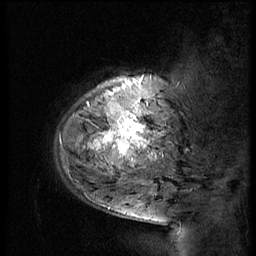
Breast MRI (dynamic contrast-enhanced), one sagittal slice; position 11 of 56 along the scan axis; 3 images stored at this slice position (order not interpretable as contrast timing); 1.5 T; TE 4.2 ms, TR 9 ms; 2.5 mm slice thickness; 256 × 256 image matrix, field of view 180 × 180 mm. Patient: female, 51 years. Case-level facts recorded for this patient, not image findings: setting: breast cancer imaged before/during neoadjuvant chemotherapy; receptor status: triple-negative.
Annotated regions visible in this slice (semi-automatically segmented with operator editing):
- analysis volume of interest (the breast-tissue region the enhancement analysis was run in; not a lesion): bounding box (x1, y1, x2, y2) in pixels: (52, 66, 183, 179)
- tumour enhancement mask (voxels above the 140 % enhancement threshold inside the analysis volume of interest): (93, 94, 145, 159)